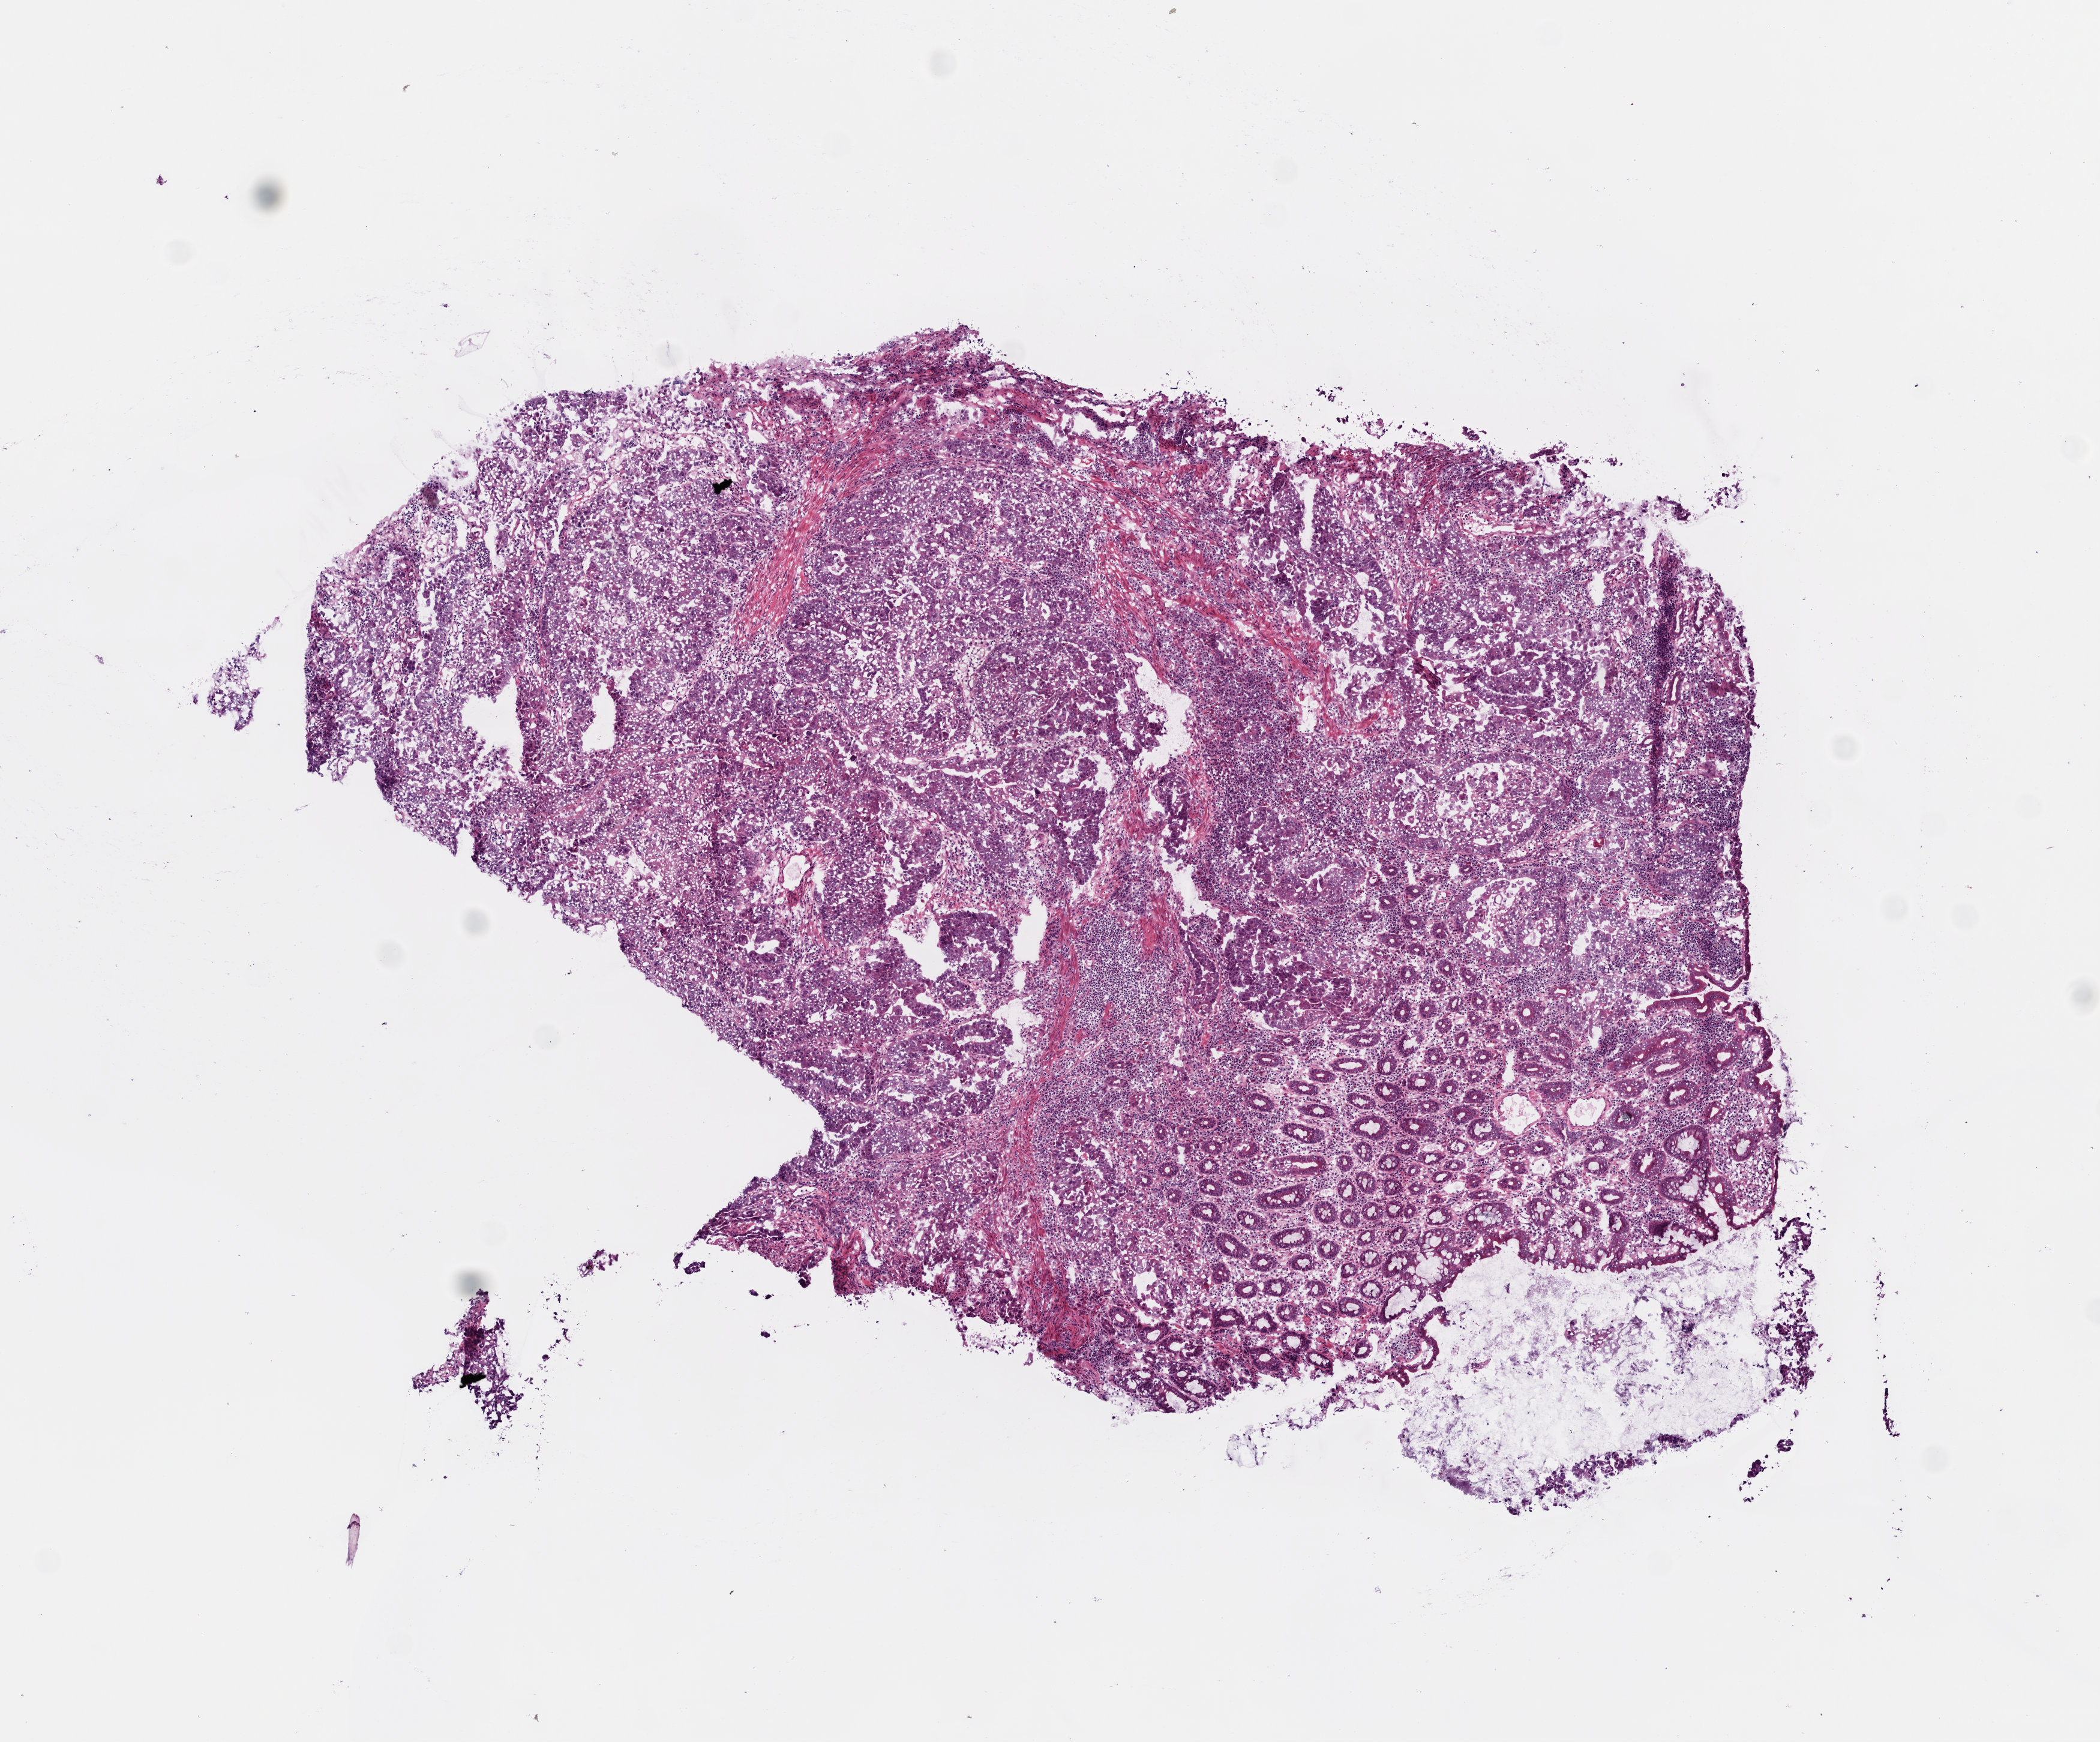
Digitized H&E tissue section (whole slide) — low-resolution overview of the scanned area, about 7.0 x 5.8 mm (acquisition: 20x scan); frozen section from the bottom of the tissue portion; sample: primary tumour, colon. Patient: female, age at initial diagnosis 50 years. Composition of this section per pathologist review: tumour cells 74%, tumour nuclei 75%, normal cells 15%, stromal cells 10%, necrosis 1%.
Lymph nodes positive (case pathology): 5 of 15 examined. Pathologic diagnosis: Adenocarcinoma, NOS (ascending colon). AJCC pathologic stage: IIIC (6th edition).